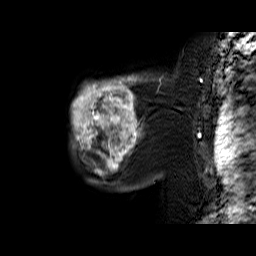
Breast MRI (dynamic contrast-enhanced), one sagittal slice. Position 50 of 60 along the scan axis. Dynamic contrast-enhanced series, time point 2 of 6 at this slice position (early post-contrast). 1.5 T. TE 6.4 ms, TR 32.9 ms. 4 mm slice thickness. 256 × 256 image matrix. Female patient. From the clinical record (not read from this slice): setting: breast cancer imaged before/during neoadjuvant chemotherapy; receptor status: triple-negative.
Annotated regions visible in this slice (semi-automatically segmented with operator editing):
- analysis volume of interest (the breast-tissue region the enhancement analysis was run in; not a lesion): box from (x=72, y=74) to (x=159, y=174) px
- tumour enhancement mask (voxels above the 100 % enhancement threshold inside the analysis volume of interest): (x=72, y=75)–(x=148, y=174)